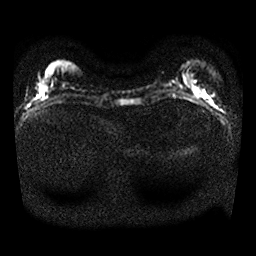
Breast MRI, one axial slice; position 7 of 25 along the scan axis; diffusion-weighted series; image 2 of 4 stored at this slice position (different b-values; order by instance number); 1.5 T; 256 × 256 image matrix, field of view 320 × 320 mm. Female patient.
Structures marked on this image (outlined manually by an expert reader):
- tumour on diffusion-weighted imaging: bounding box <202,93,209,99> (left, top, right, bottom; pixels)